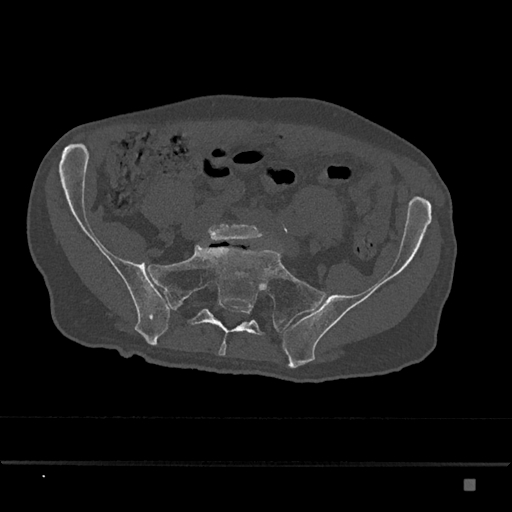
CT including the spine, one axial slice. Position 214 of 797 along the scan axis. 120 kVp. Bone window (W 1800 / L 400 HU). 0.5 mm slice thickness. 512 × 512 image matrix, field of view 390 × 390 mm. Male patient, age 72 years. Case-level facts recorded for this patient, not image findings: primary cancer: prostate.
Structures marked on this image (semi-automatically segmented with operator editing):
- L5 vertebra: box from (x=208, y=224) to (x=263, y=242) px